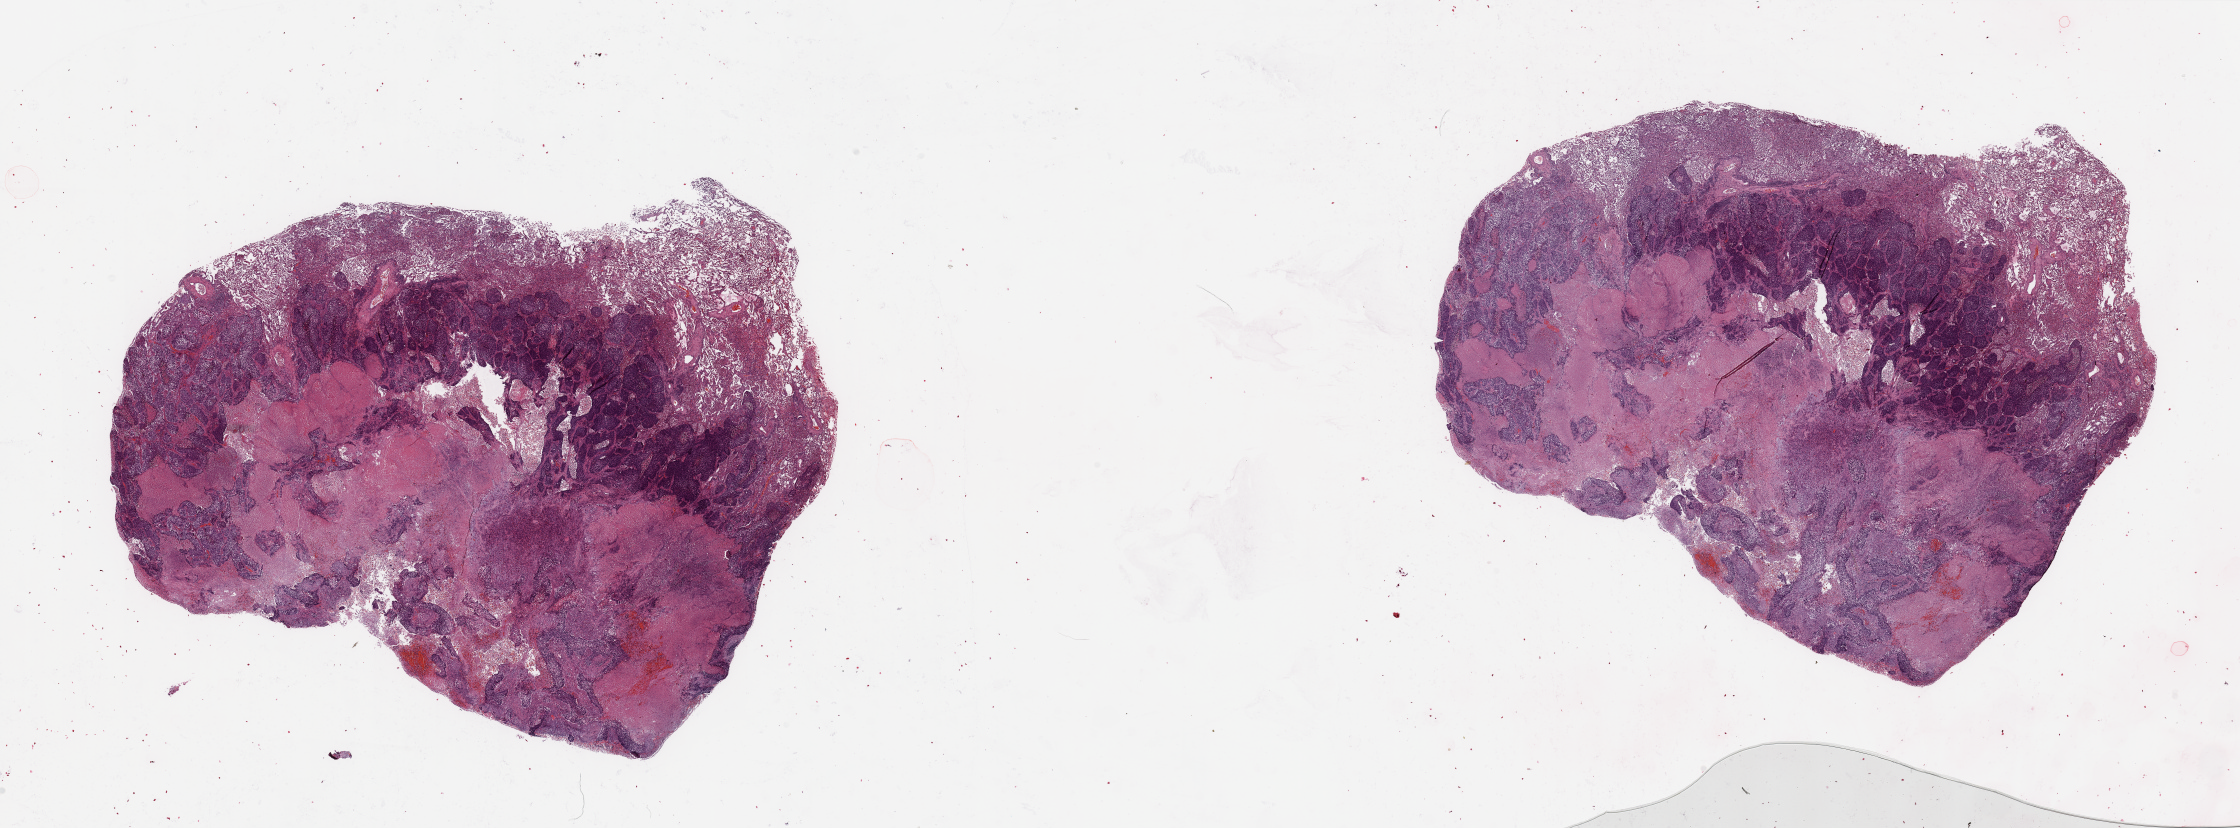
H&E-stained whole-slide image — a low-resolution overview of the entire scanned area, about 35.4 x 13.1 mm (from a 20x scan). Lung, tumour tissue. 54-year-old male patient. Histologic grade: G2 (moderately differentiated).
* AJCC pathologic stage: IIIA
* diagnosis: Squamous cell carcinoma, NOS